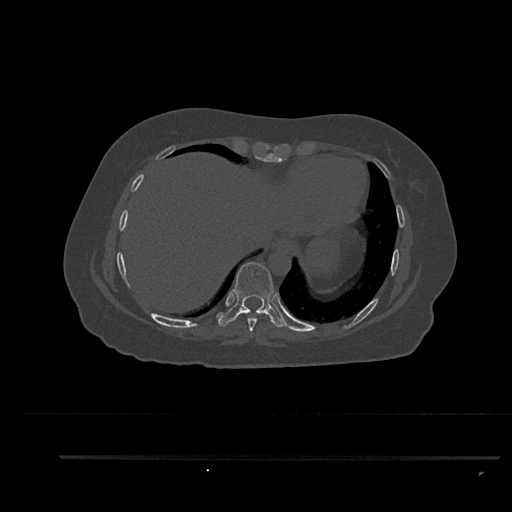
CT including the spine, one axial slice; position 429 of 797 along the scan axis; reconstruction kernel Br40s/3; 120 kVp; bone window (W 1800 / L 400 HU); 512 × 512 image matrix. Patient: female, 44 years. From the clinical record (not read from this slice): primary cancer: renal.
Outlined on this slice (semi-automatically segmented with operator editing):
- T8 vertebra: bounding box (x1, y1, x2, y2) in pixels: (246, 310, 262, 332)
- T9 vertebra: (218, 262, 284, 328)